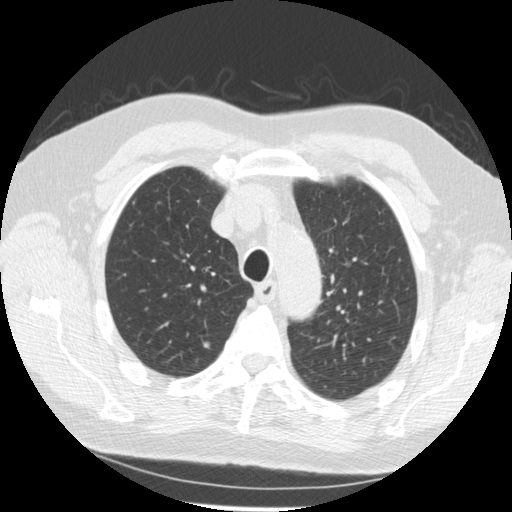
Low-dose screening chest CT, one axial slice. Slice 206 of 259 in the series (ordered by position). Lung window (W 1500 / L -600 HU). 2.5 mm slice thickness. 512 × 512 image matrix.
Outlined on this slice (expert manual segmentation):
- lesion 1 (nodule, upper lobe of right lung): bounding box [x1, y1, x2, y2] px = [202, 342, 210, 350]